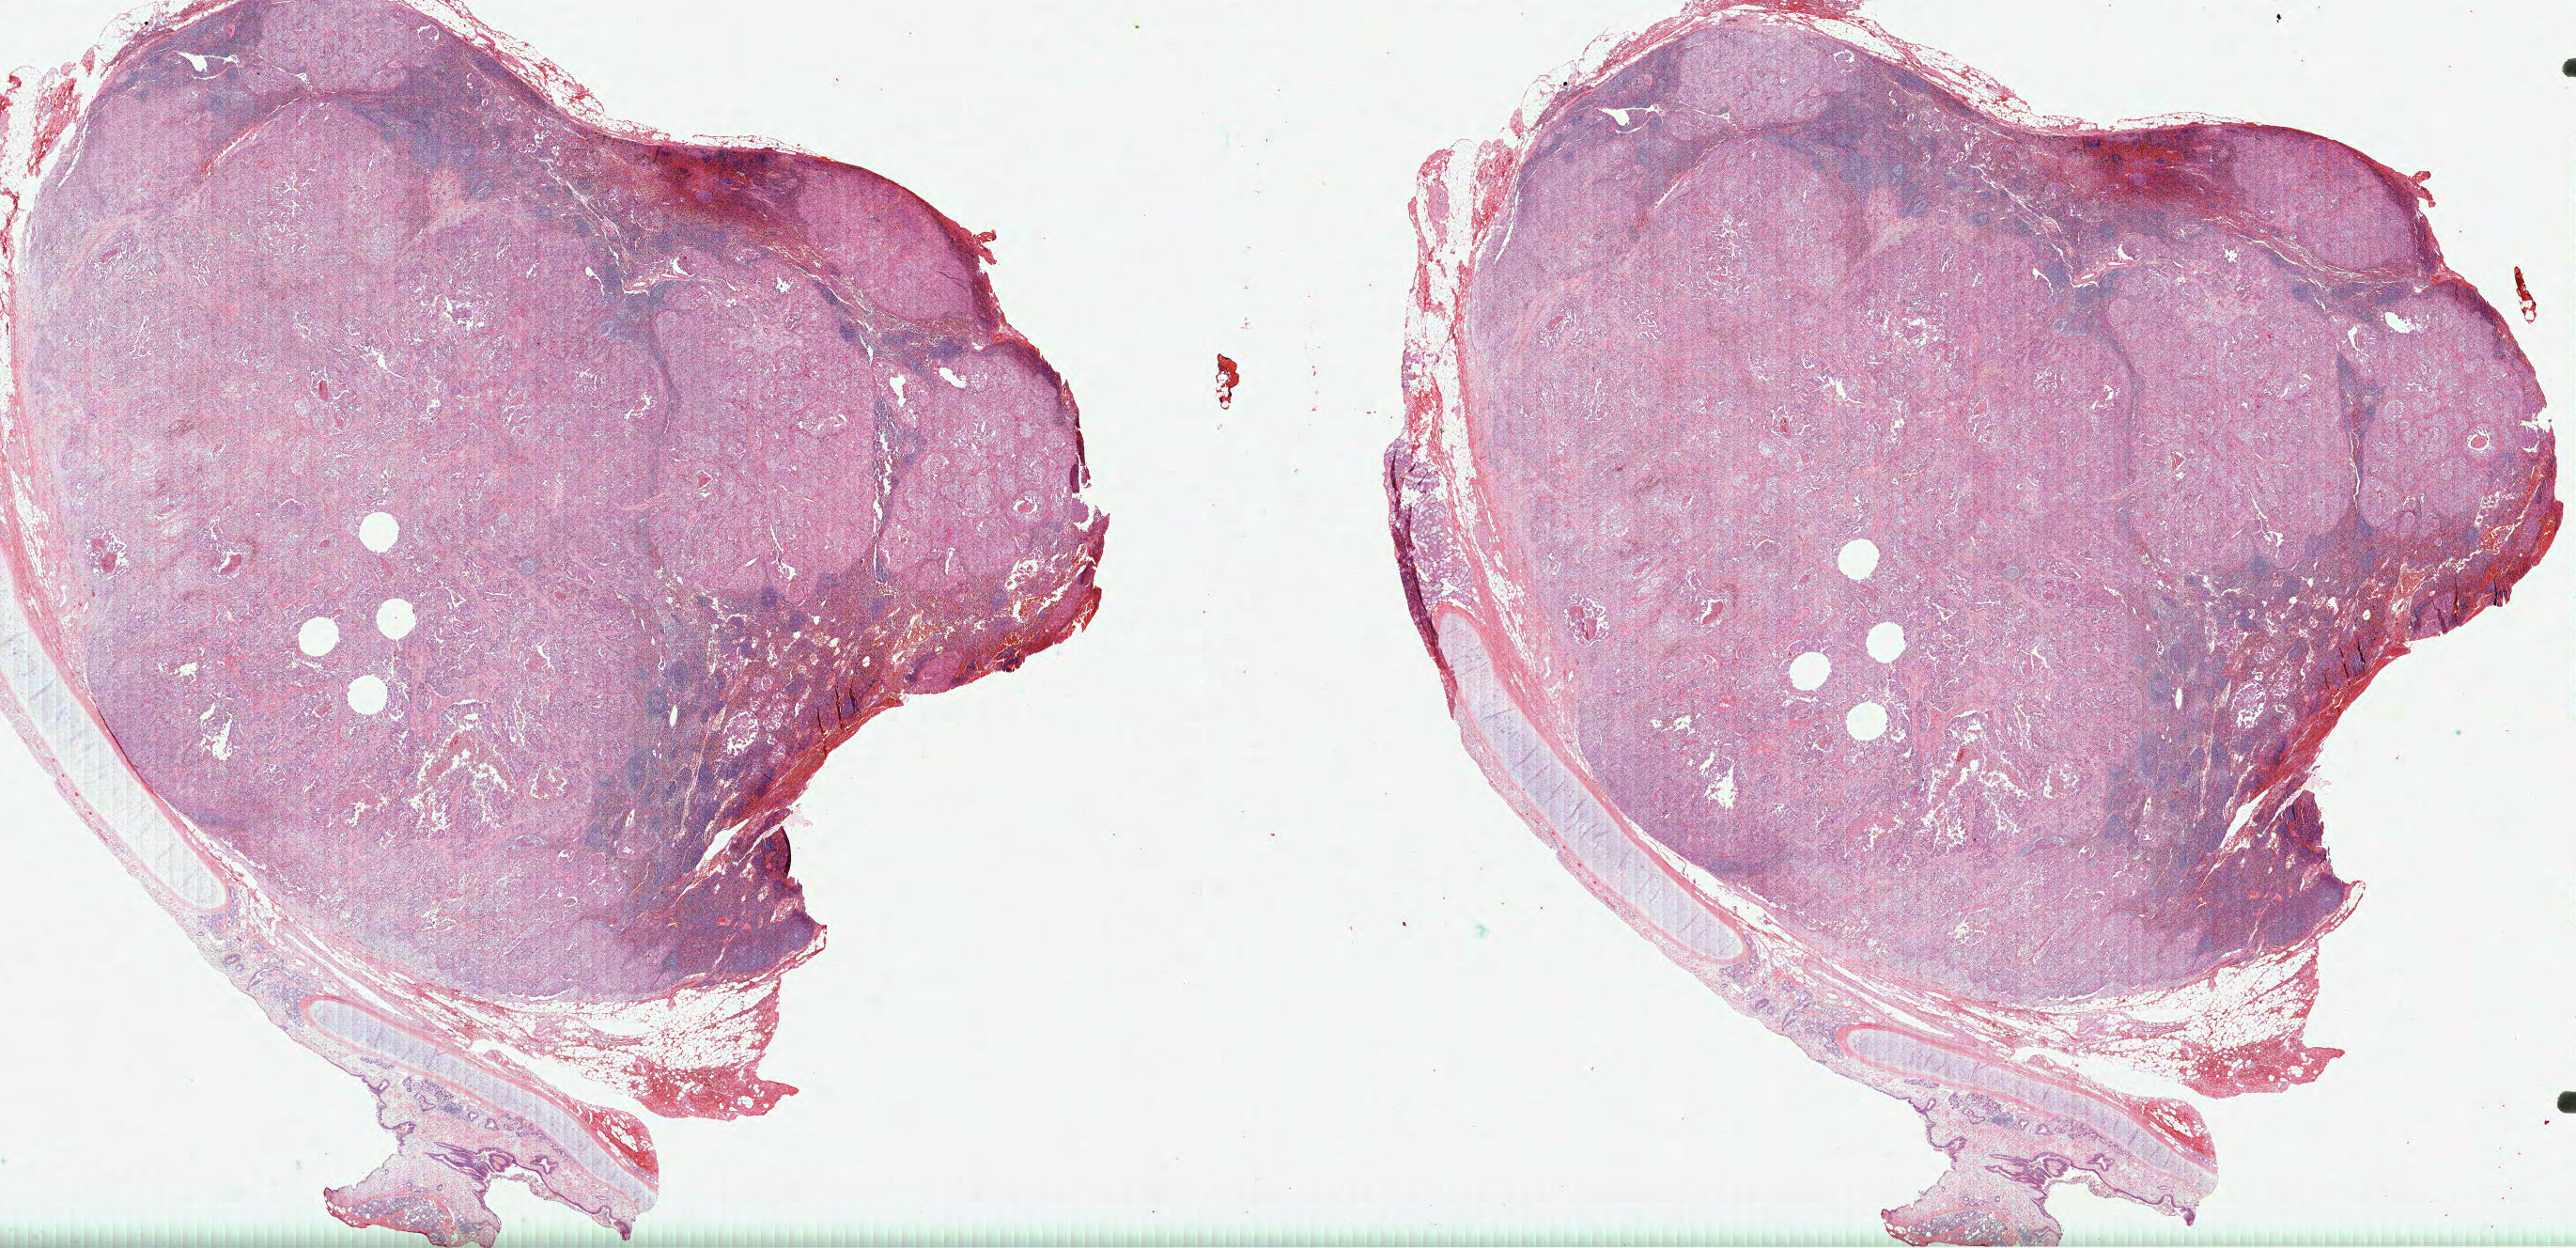
Hematoxylin and eosin (H&E) stained whole-slide image, a low-resolution overview of the entire scanned area, about 44.2 x 21.4 mm, FFPE section, primary tumour sample from the lung. Patient: male, age at initial diagnosis 45 years.
Diagnosis: Adenocarcinoma, NOS (upper lobe, lung). AJCC pathologic stage: IIA.